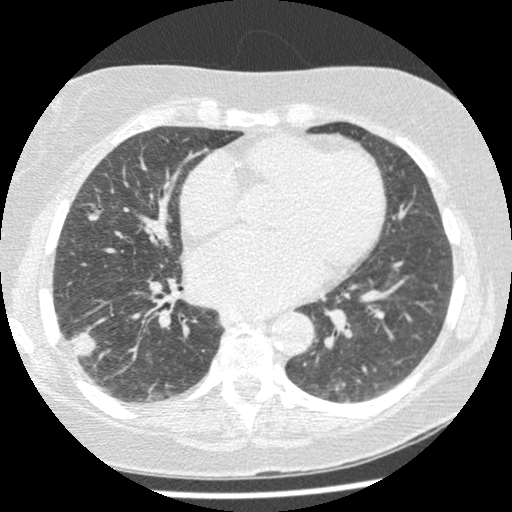
Low-dose screening chest CT, one axial slice. Position 111 of 241 along the scan axis. 120 kVp. Lung window (W 1500 / L -600 HU). 512 × 512 image matrix, field of view 305 × 305 mm.
Annotated regions visible in this slice (manually delineated by an expert):
- lesion 1 (tumor, lower lobe of right lung): bounding box (x1, y1, x2, y2) in pixels: (72, 333, 96, 359)